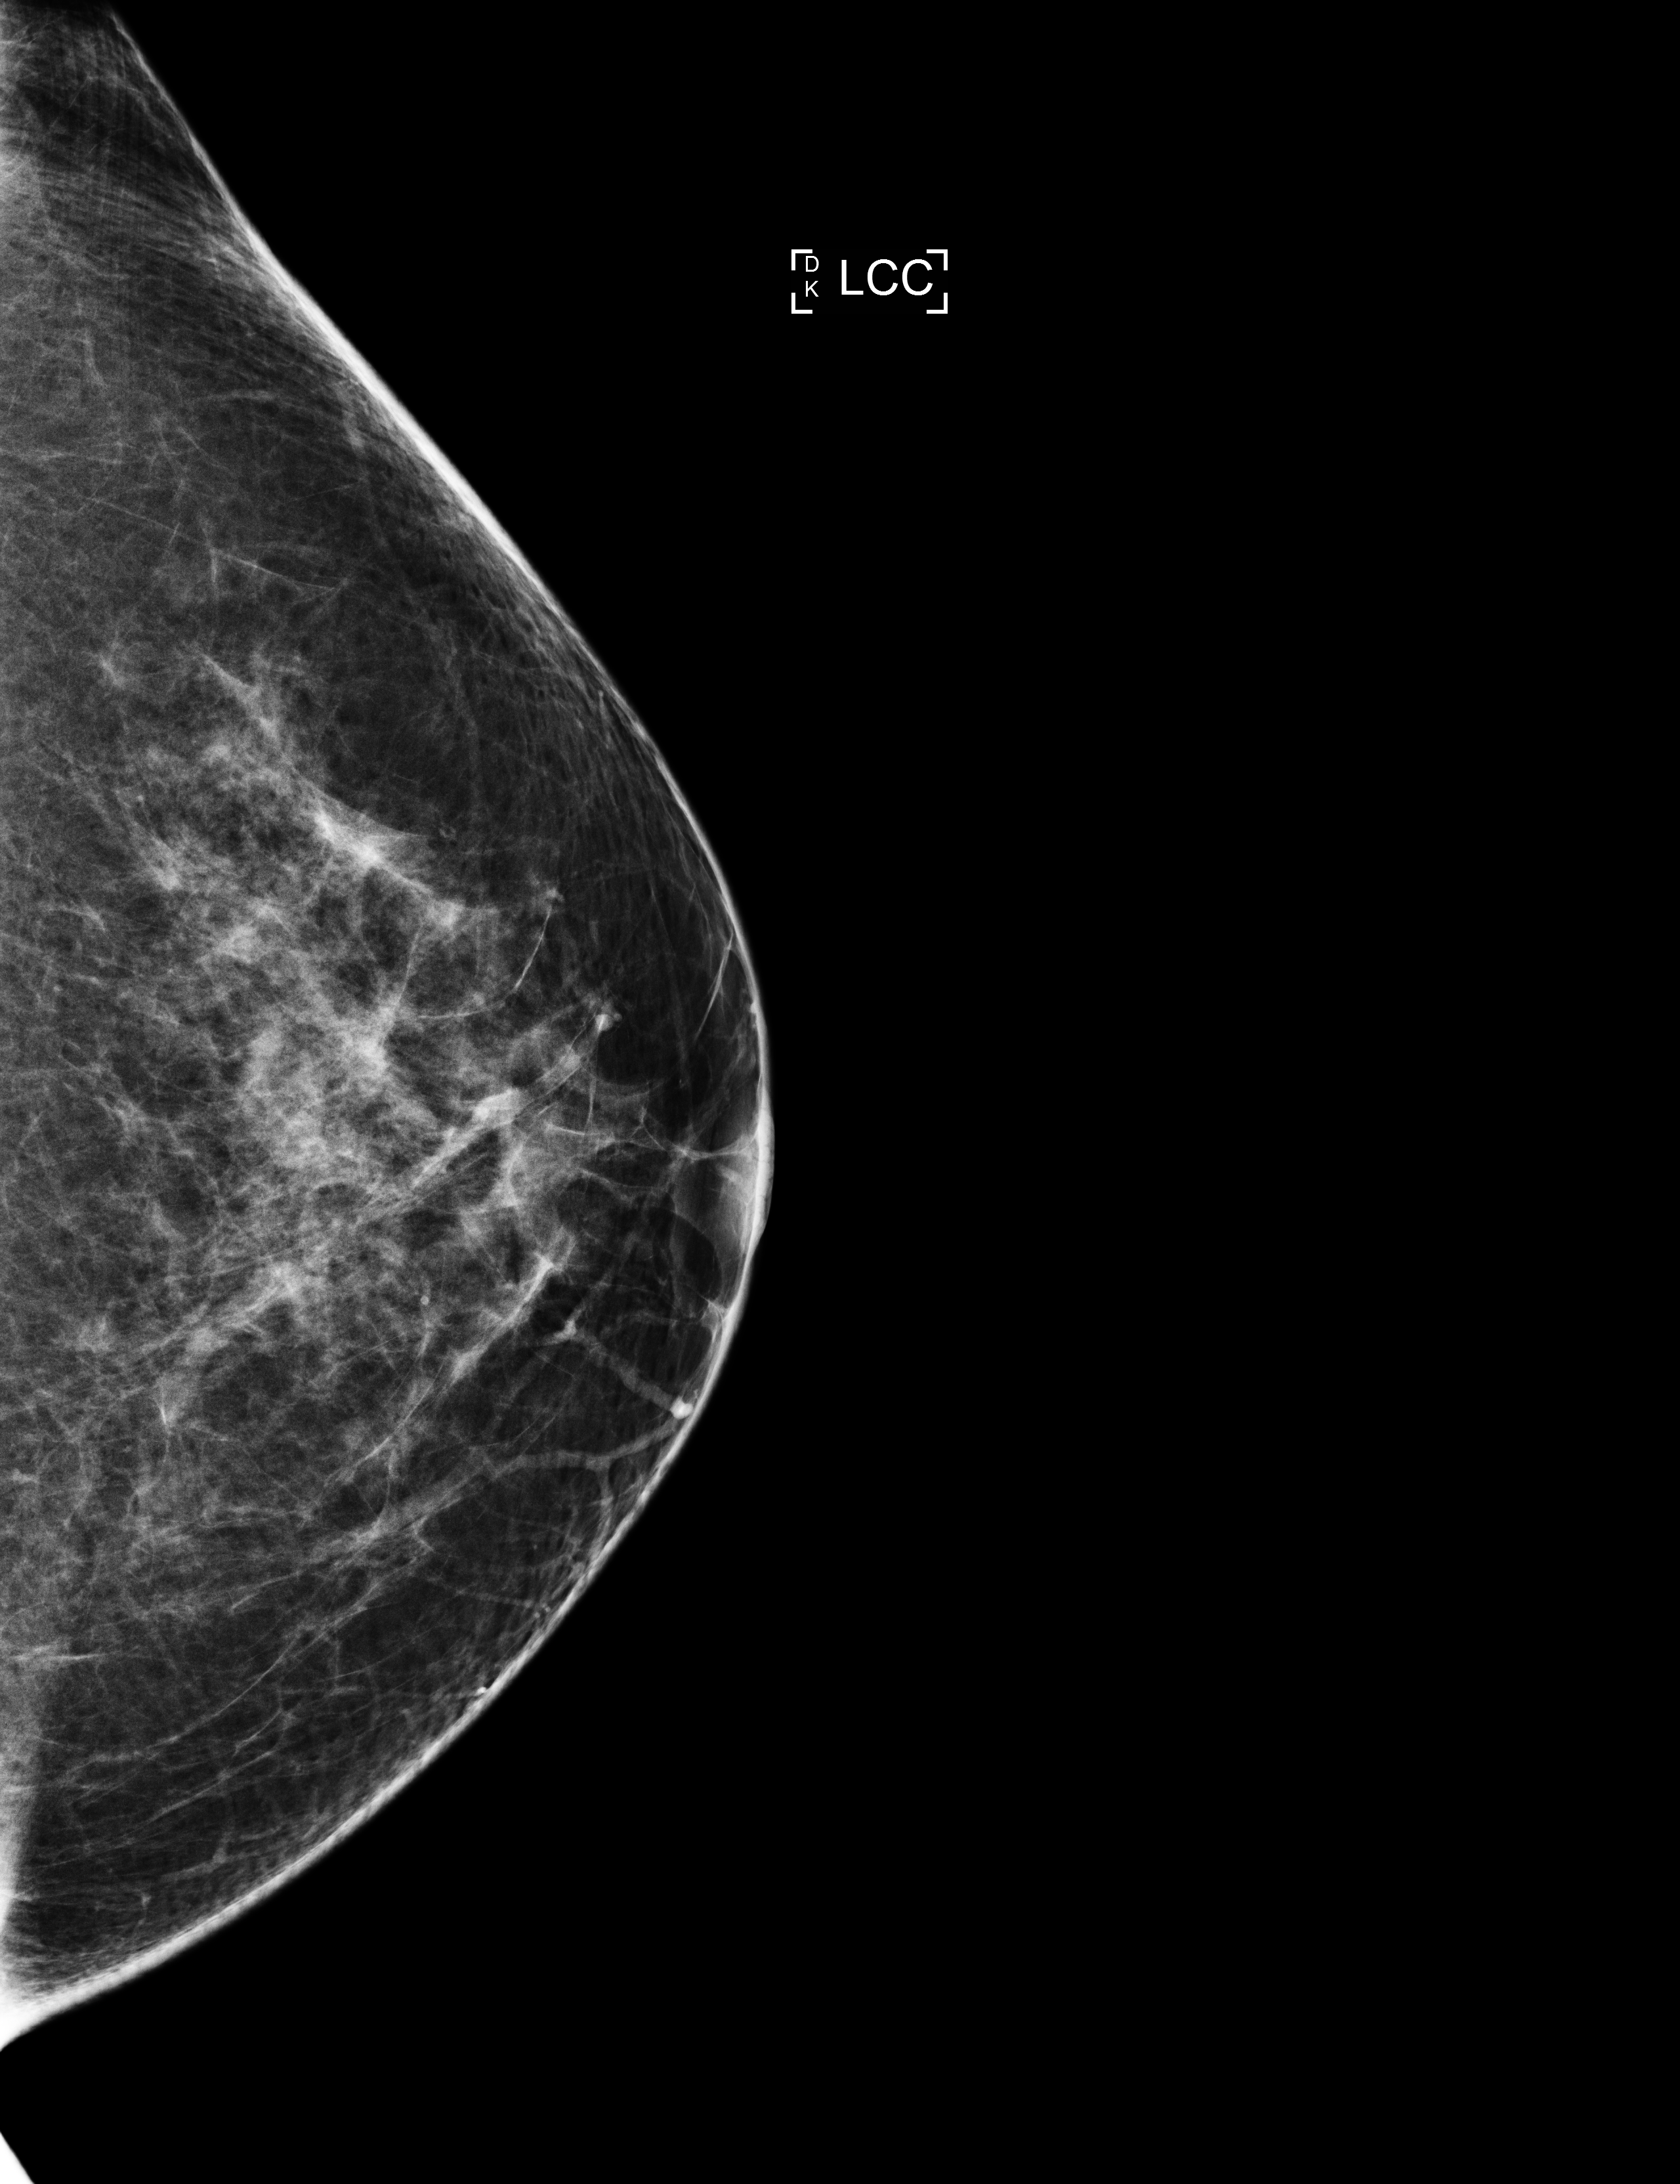
Screening examination, compressed breast thickness 61 mm. Female patient, age 46 years.
Image type: full-field digital mammogram. Breast: left. Projection: CC view.